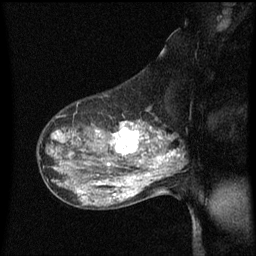
Breast MRI (dynamic contrast-enhanced), one sagittal slice; position 40 of 60 along the scan axis; dynamic contrast-enhanced series, image 2 of 3 at this slice position (ordered by acquisition); 1.5 T; TE 4.2 ms, TR 8.4 ms; 2 mm slice thickness; 256 × 256 image matrix. Female patient, age 50 years.
Outlined on this slice (semi-automatic segmentation, software-assisted and operator-edited):
- analysis volume of interest (the breast-tissue region the enhancement analysis was run in; not a lesion): box from (x=100, y=122) to (x=153, y=171) px
- tumour enhancement mask (voxels above the 70 % enhancement threshold inside the analysis volume of interest): (x=107, y=122)–(x=151, y=167)